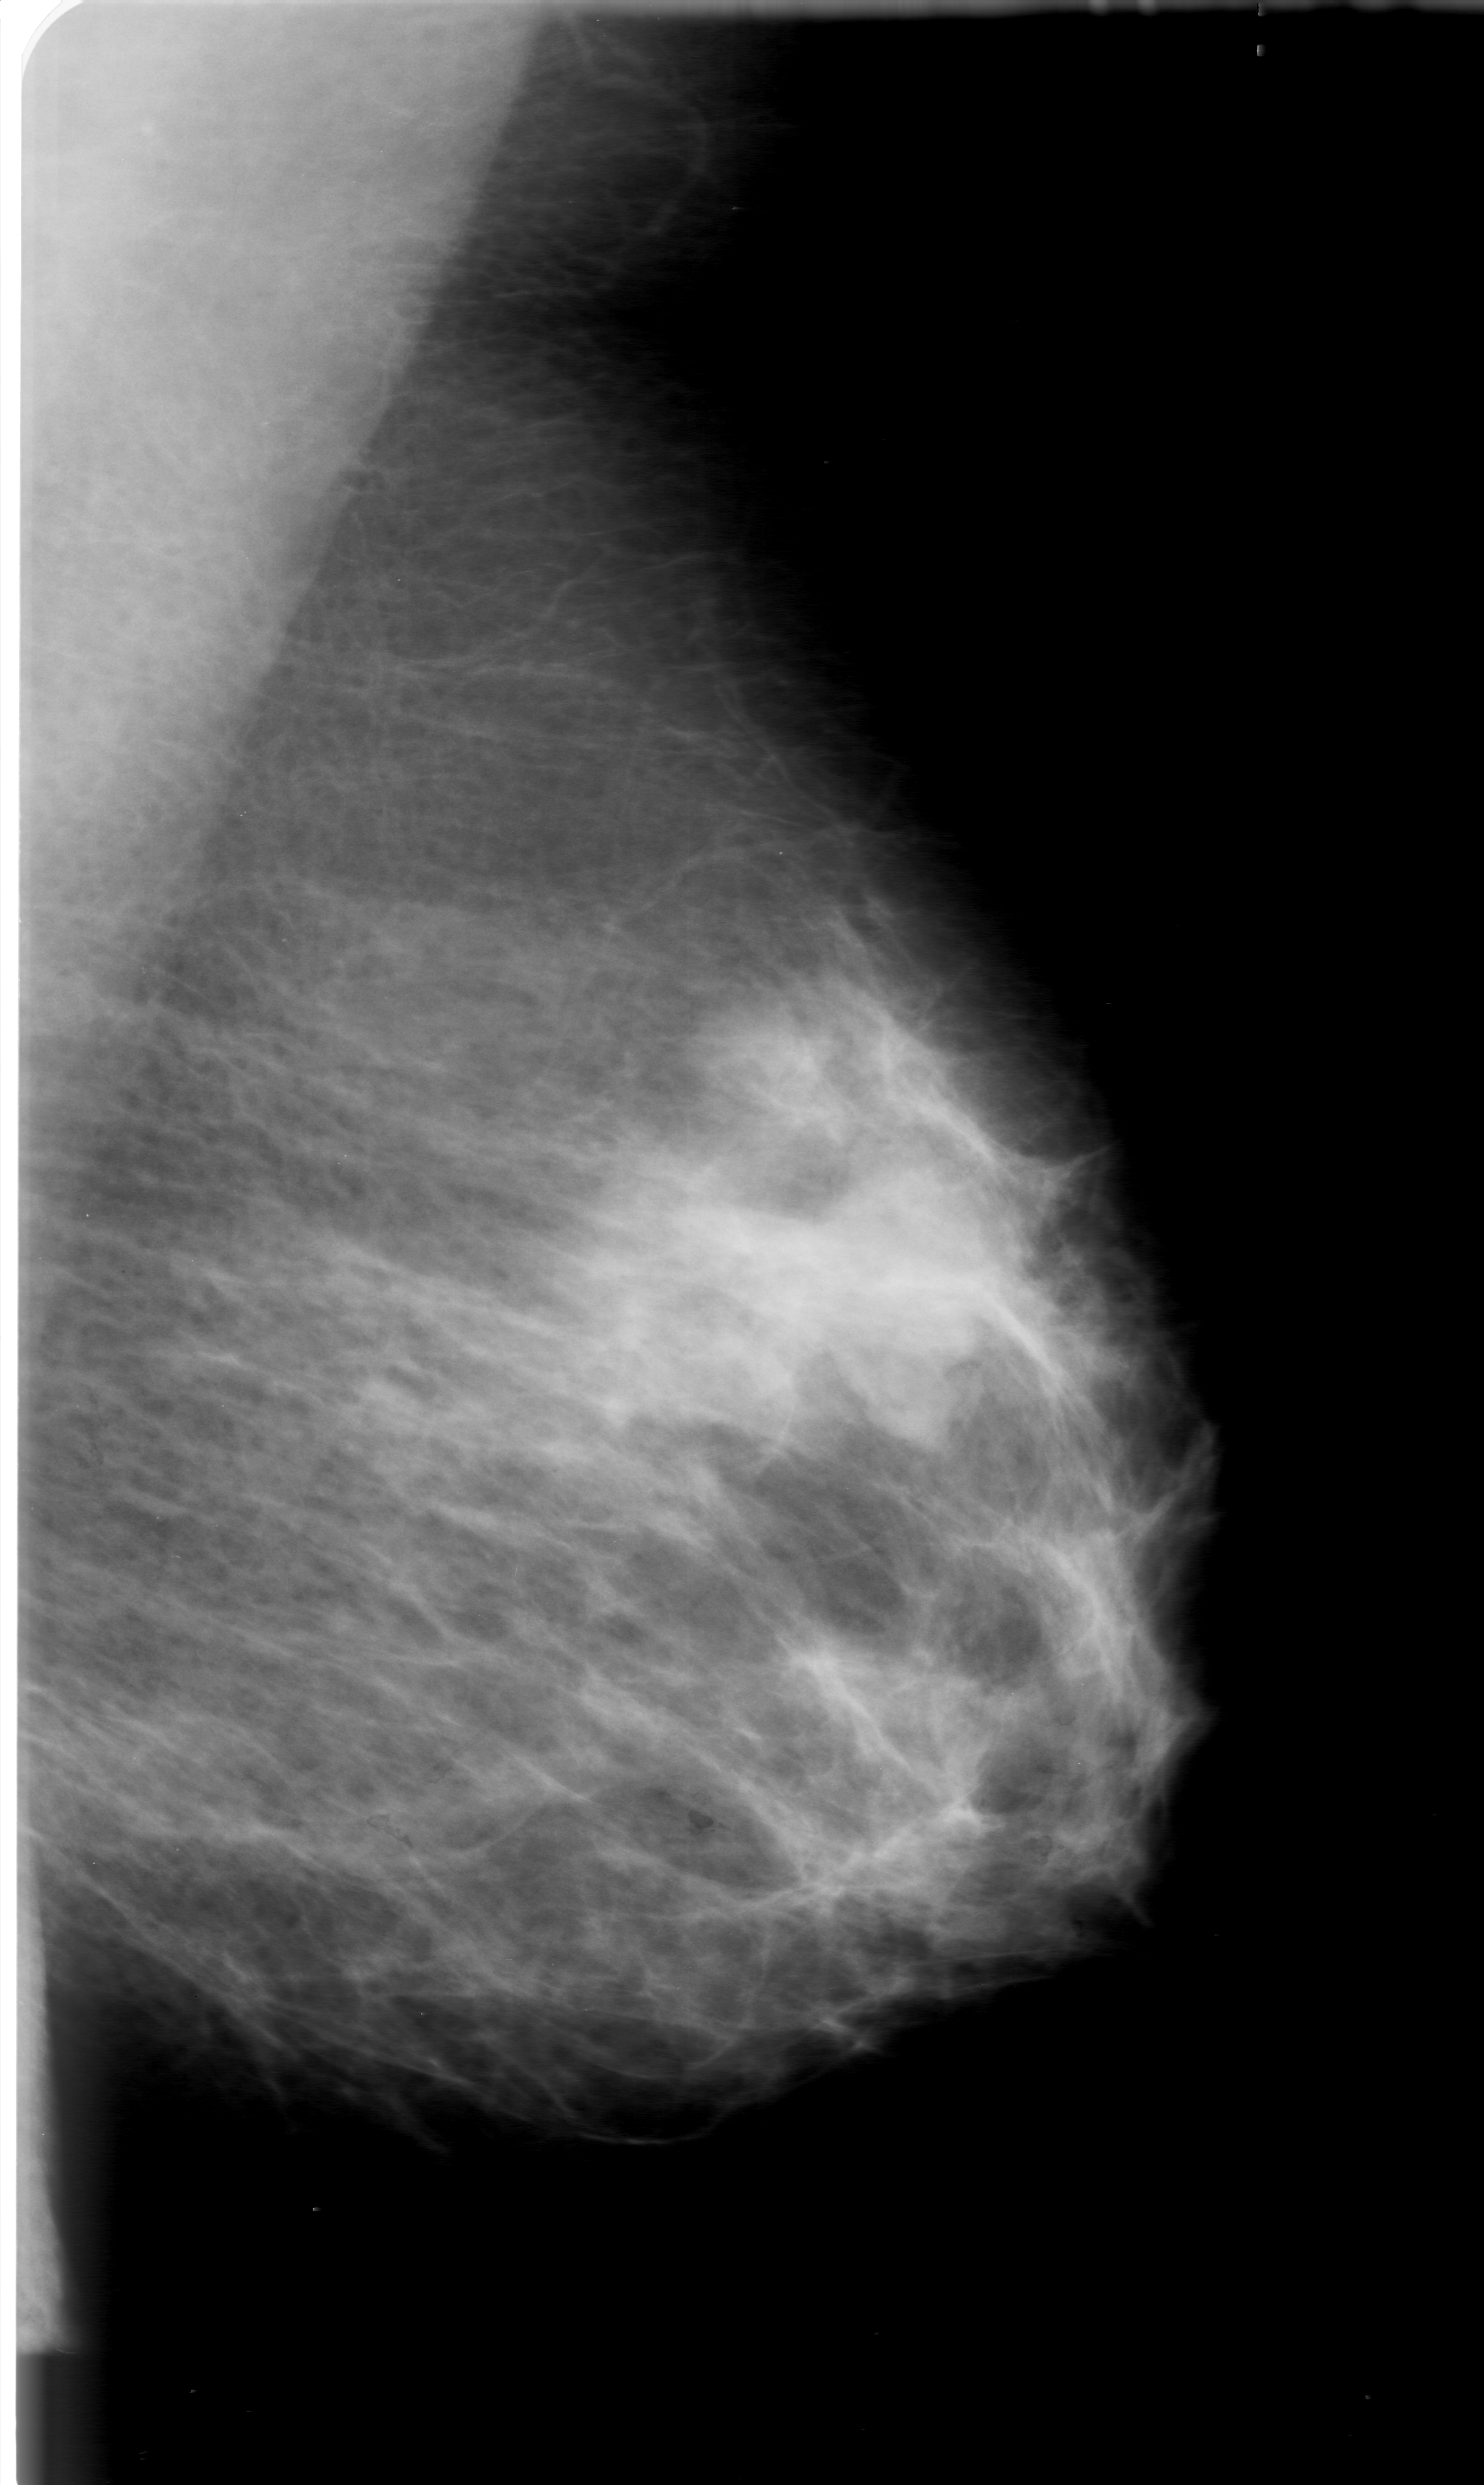
Digitized screen-film mammogram. Left breast. MLO view. Breast composition: heterogeneously dense (BI-RADS density category 3 of 4). 1484 × 2485 image matrix.
Marked abnormalities (boxes around the expert regions of interest):
- mass, shape lobulated, margins circumscribed; BI-RADS assessment category 0; pathology (as recorded): benign: bounding box [x1, y1, x2, y2] px = [819, 1161, 984, 1380]